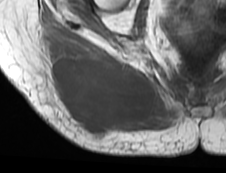
MRI of an extremity soft-tissue mass, one axial slice. Slice 31 of 73 in the series (ordered by position). MR volume resampled by the dataset authors to the PET/CT grid (not the native acquisition matrix). 226 × 173 image matrix, field of view 221 × 169 mm. Female patient. From the clinical record (not read from this slice): histological type: spindle cell suggestive of myxofibrosarcoma; grade: intermediate; site of the primary tumour: right buttock.
Outlined on this slice (expert contour drawn on MRI and transferred to this co-registered scan by the dataset authors):
- gross tumour volume (mass): bounding box [x1, y1, x2, y2] px = [50, 42, 156, 139]